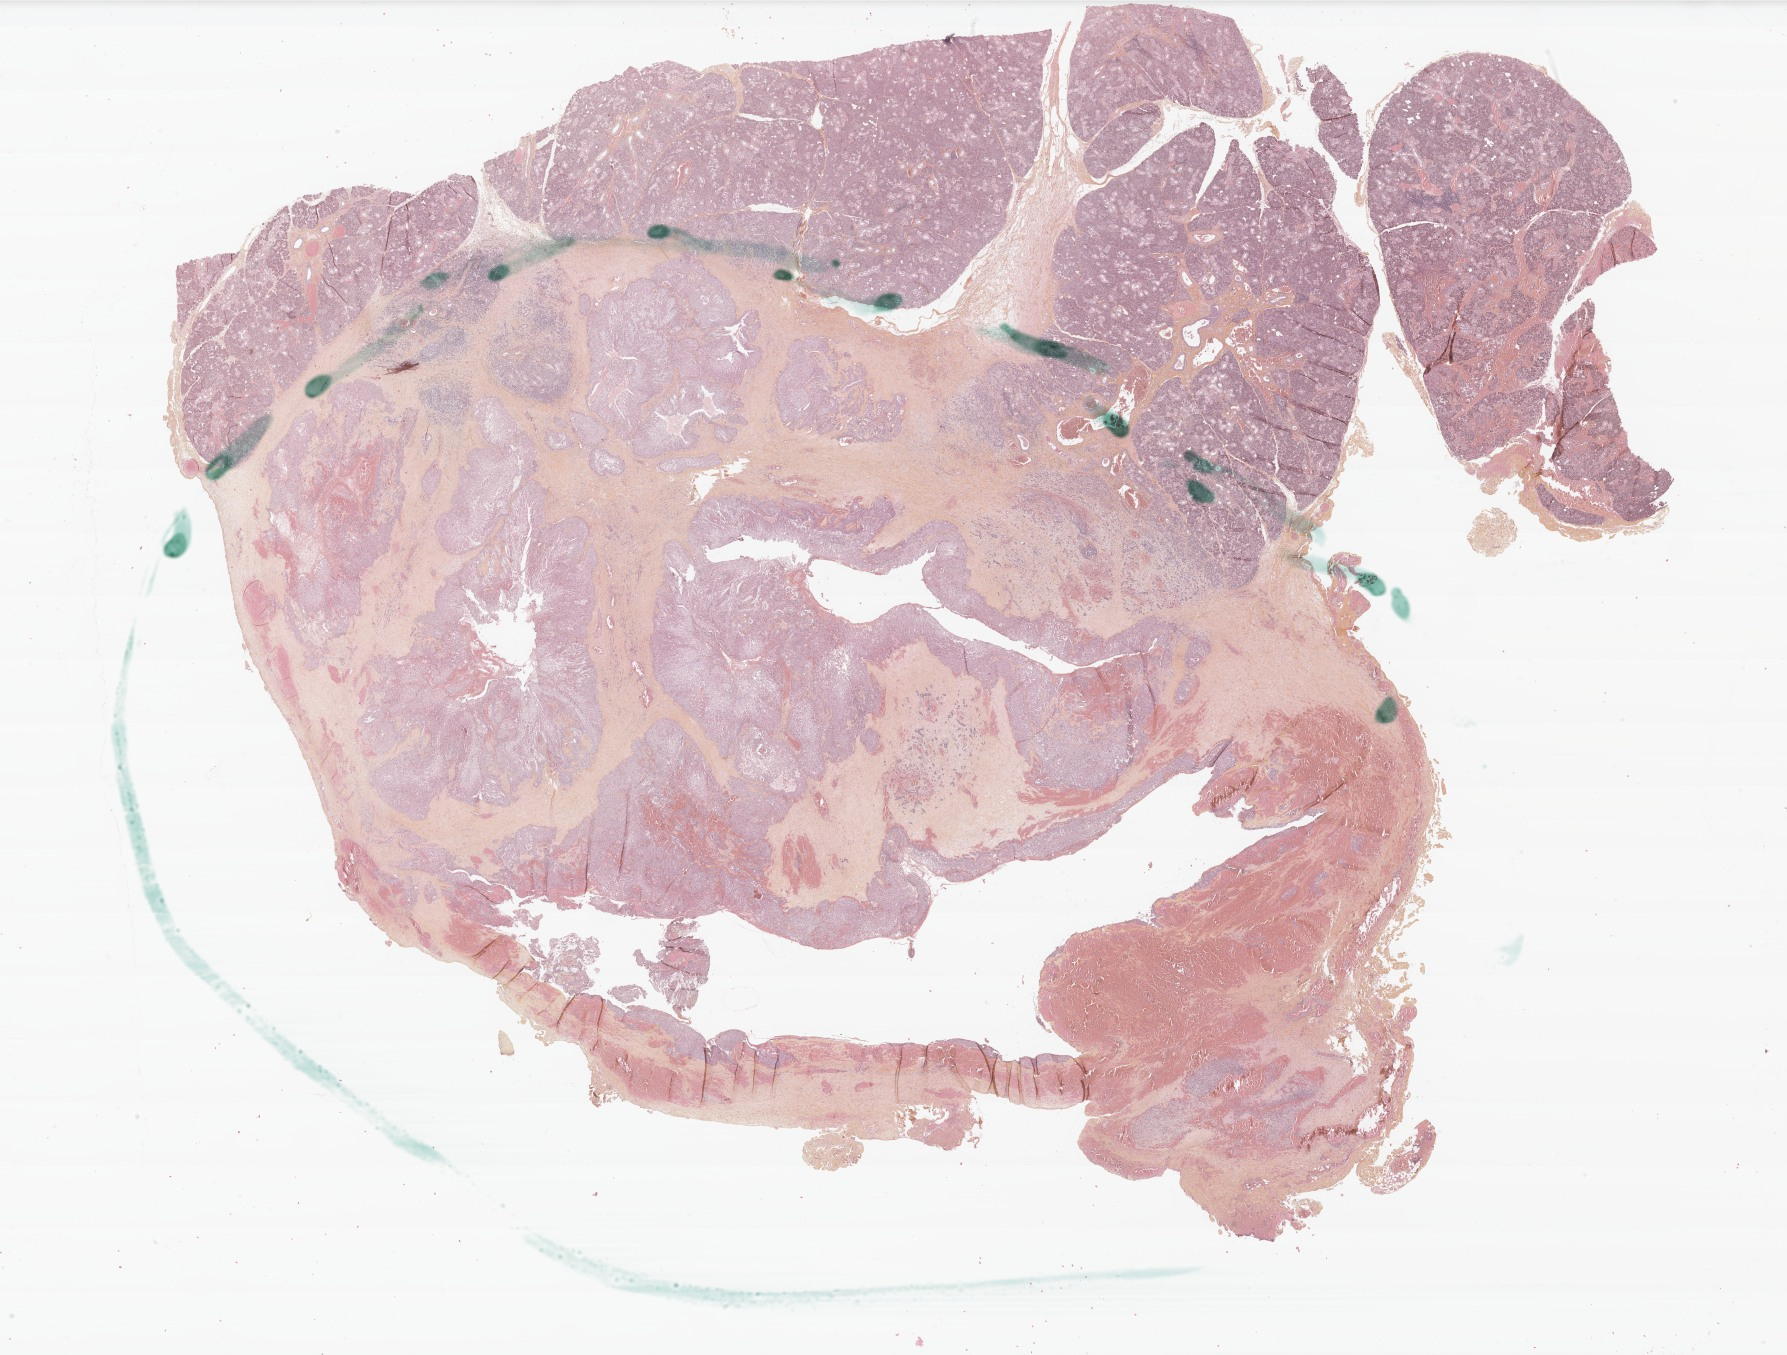
H&E whole-slide image of tumor tissue from the submandibular gland — low-resolution overview of the scanned area, about 30.1 x 22.8 mm; formalin-fixed, paraffin-embedded (FFPE) tissue. Patient male; age 195 months (16 years 3 months).
- diagnosis (ICD-O-3 morphology term): Mucoepidermoid carcinoma